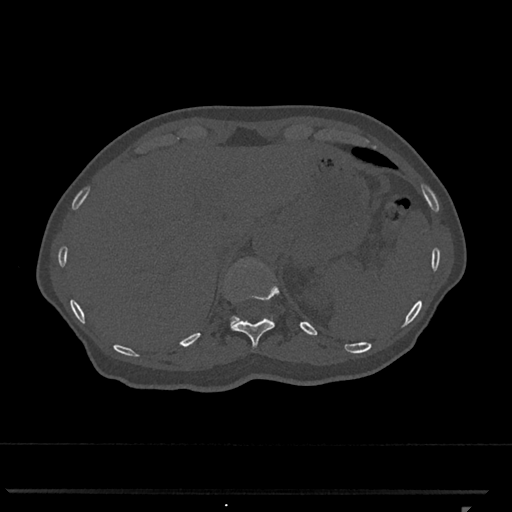
CT including the spine, one axial slice. Slice 503 of 793 in the series (ordered by position). 120 kVp. Bone window (W 1800 / L 400 HU). 0.5 mm slice thickness. 512 × 512 image matrix, field of view 380 × 380 mm. Female patient, age 62 years. From the clinical record (not read from this slice): primary cancer: renal.
Outlined on this slice (semi-automatically segmented with operator editing):
- T11 vertebra: bounding box (x1, y1, x2, y2) in pixels: (230, 261, 279, 349)
- T12 vertebra: (230, 264, 273, 325)